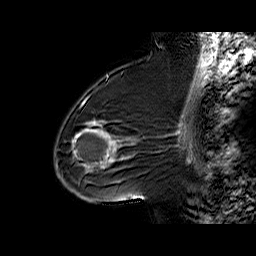
Breast MRI (dynamic contrast-enhanced), one sagittal slice; slice 37 of 60 in the series (ordered by position); dynamic contrast-enhanced series, time point 2 of 6 at this slice position (early post-contrast); 1.5 T; TE 6.3 ms, TR 32.4 ms; 256 × 256 image matrix, field of view 200 × 200 mm. Female patient. From the clinical record (not read from this slice): setting: breast cancer imaged before/during neoadjuvant chemotherapy; receptor status: triple-negative.
Annotated regions visible in this slice (semi-automatic segmentation, software-assisted and operator-edited):
- analysis volume of interest (the breast-tissue region the enhancement analysis was run in; not a lesion): bounding box [x1, y1, x2, y2] px = [65, 88, 154, 187]
- tumour enhancement mask (voxels above the 100 % enhancement threshold inside the analysis volume of interest): [72, 121, 116, 168]